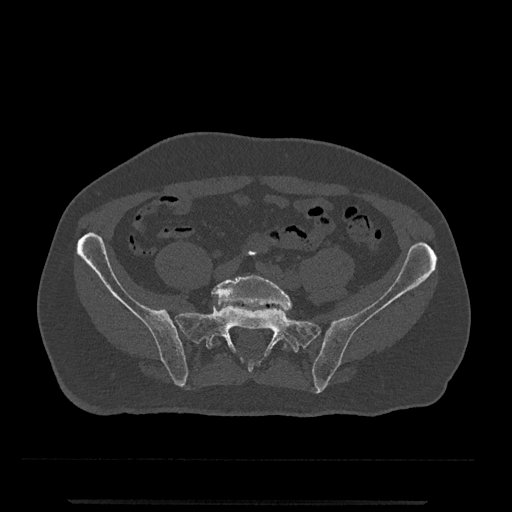
CT including the spine, one axial slice; position 33 of 797 along the scan axis; reconstruction kernel Br40s/3; 120 kVp; bone window (W 1800 / L 400 HU); 0.5 mm slice thickness; 512 × 512 image matrix, field of view 419 × 419 mm. Male patient, age 63 years. From the clinical record (not read from this slice): primary cancer: prostate.
Annotated regions visible in this slice (semi-automatic segmentation, software-assisted and operator-edited):
- L5 vertebra: bounding box (x1, y1, x2, y2) in pixels: (212, 274, 293, 350)